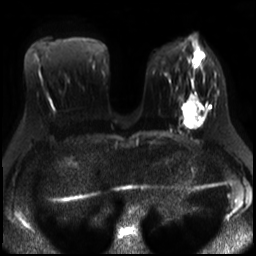
Breast MRI, one axial slice. Slice 12 of 30 in the series (ordered by position). Diffusion-weighted series; image 2 of 4 stored at this slice position (different b-values; order by instance number). 3 T. 256 × 256 image matrix. Female patient.
Outlined on this slice (outlined manually by an expert reader):
- tumour on diffusion-weighted imaging: bounding box <182,97,200,121> (left, top, right, bottom; pixels)